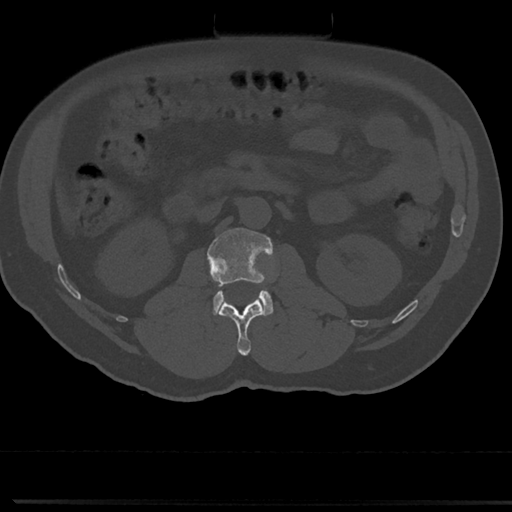
CT including the spine, one axial slice. Position 44 of 817 along the scan axis. Reconstruction kernel Br40s/3. 120 kVp. Bone window (W 1800 / L 400 HU). 0.5 mm slice thickness. 512 × 512 image matrix. Male patient, age 61 years. From the clinical record (not read from this slice): primary cancer: prostate.
Annotated regions visible in this slice (semi-automatic segmentation, software-assisted and operator-edited):
- L1 vertebra: bounding box <219,299,264,355> (left, top, right, bottom; pixels)
- L2 vertebra: <208,227,273,316>